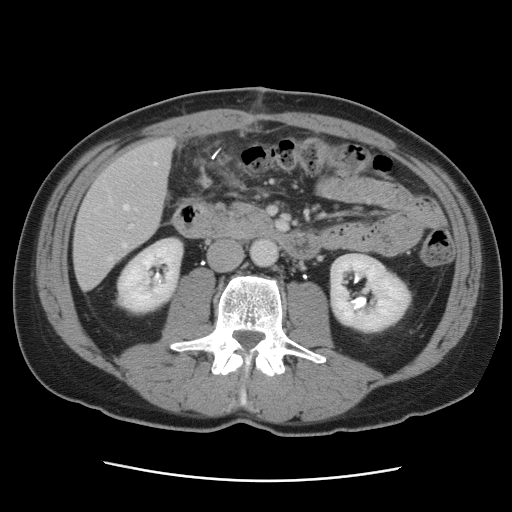
Contrast-enhanced abdominal CT, one axial slice; slice 26 of 89 in the series (ordered by position); intravenous contrast given; soft-tissue window (W 400 / L 40 HU); 5 mm slice thickness; 512 × 512 image matrix. Male patient, age 59 years. From the clinical record (not read from this slice): diagnosis: colorectal cancer liver metastases, imaged before liver resection; multiple liver metastases: yes; largest metastasis: 0.6 cm; disease in both lobes: yes.
Outlined on this slice (outlined manually by an expert reader):
- hepatic veins: bounding box <90,162,157,260> (left, top, right, bottom; pixels)
- liver: <74,140,174,289>
- planned liver remnant (the part of the liver to remain after resection): <75,140,174,248>
- portal vein (with intrahepatic branches): <129,225,133,229>